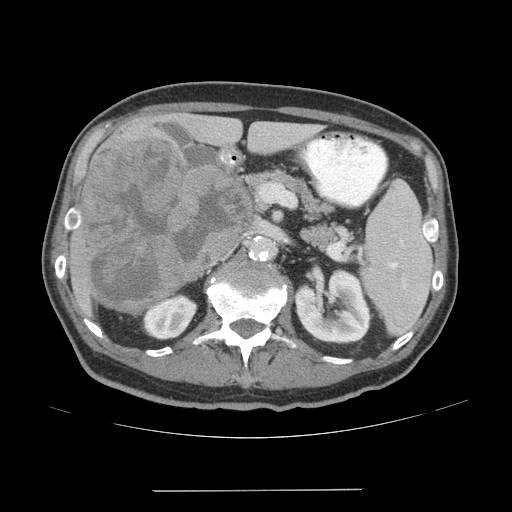
Contrast-enhanced abdominal CT (liver protocol), one axial slice. Position 24 of 77 along the scan axis. Reconstruction kernel STANDARD. 140 kVp. Soft-tissue window (W 400 / L 40 HU). 2.5 mm slice thickness. 512 × 512 image matrix. From the clinical record (not read from this slice): diagnosis: hepatocellular carcinoma (patient treated with transarterial chemoembolisation; whether this scan precedes or follows treatment is not stated here); TNM stage (as recorded): Stage-IVA; Child-Pugh class: A; tumour differentiation: well differentiated; tumour nodularity: uninodular.
Structures marked on this image (semi-automatic segmentation, software-assisted and operator-edited):
- liver parenchyma outside the tumour (the mass and vessels are separate outlines, so this box may not span the whole liver): box from (x=70, y=112) to (x=318, y=314) px
- mass: (x=80, y=139)–(x=254, y=314)